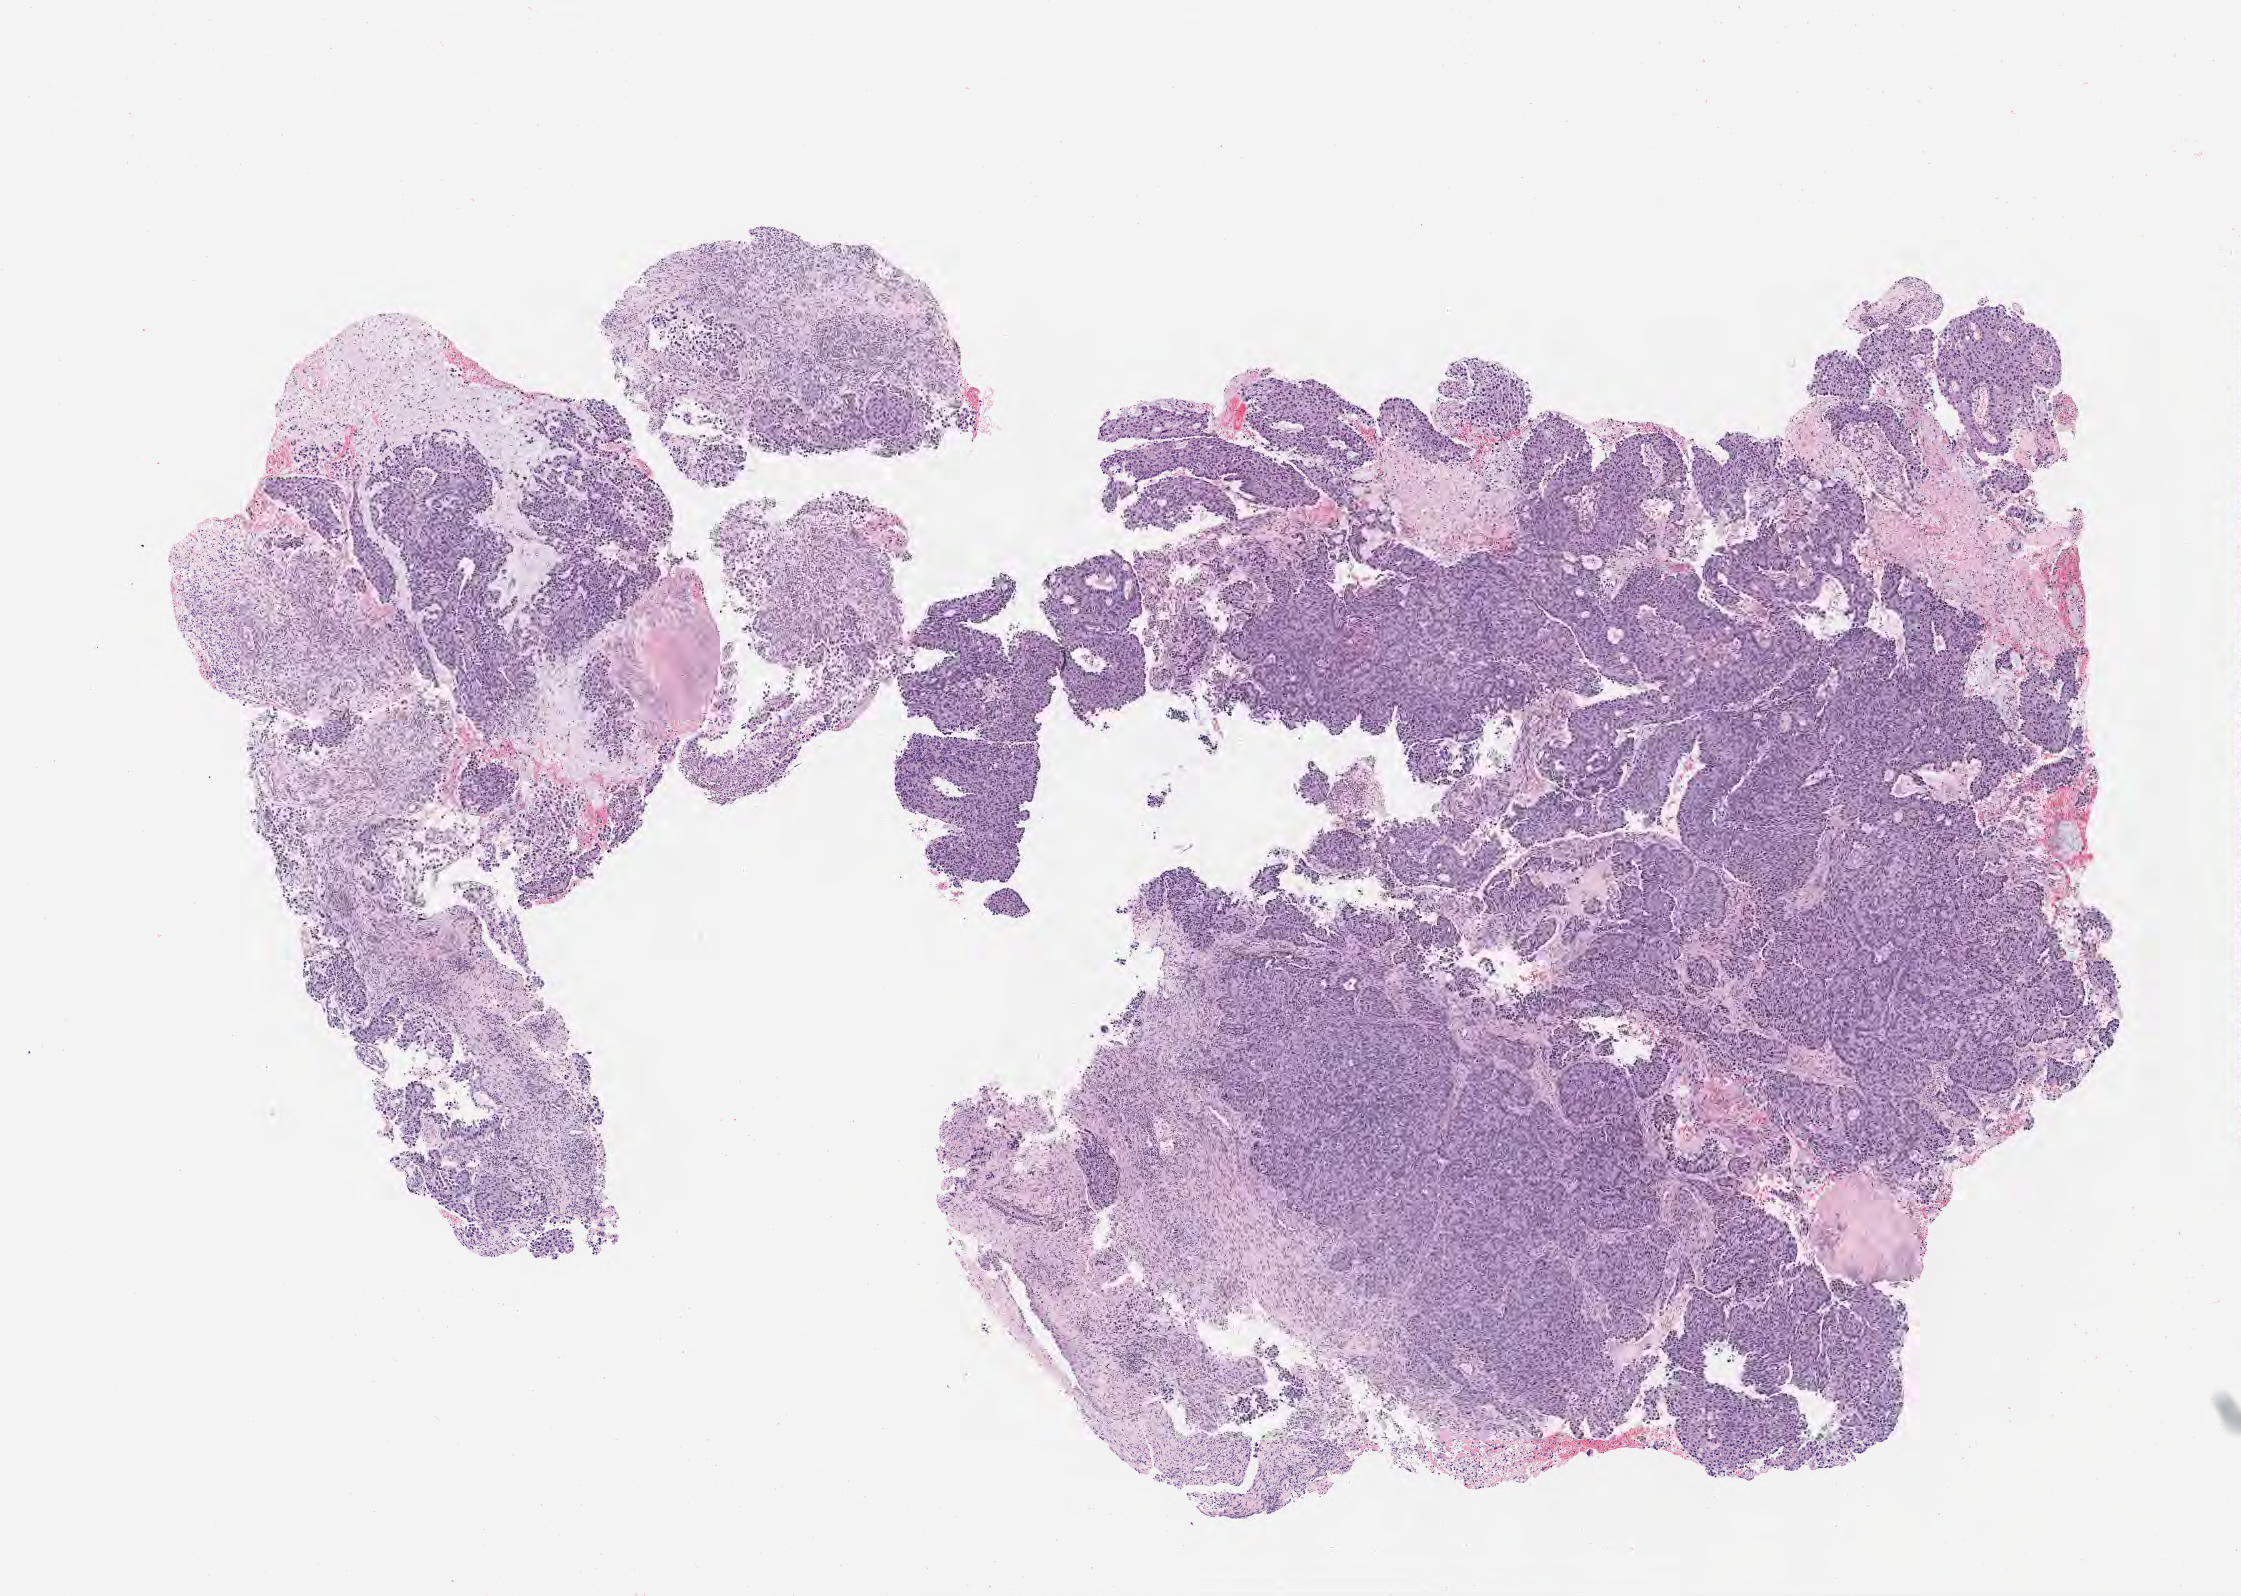
Digitized hematoxylin and eosin (H&E)-stained section, shown as a low-resolution overview of the whole scanned area (about 9.1 x 6.4 mm). Specimen: tumor tissue. Anatomic site: cervix. Patient female; 40 years old.
Diagnosis: Adenocarcinoma, NOS.